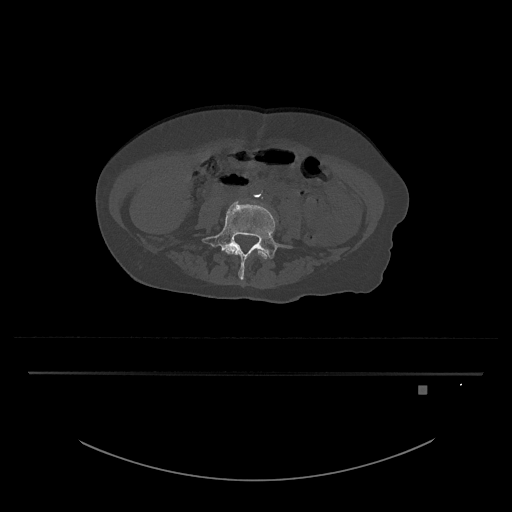
CT including the spine, one axial slice; position 319 of 797 along the scan axis; reconstruction kernel Br40s/3; bone window (W 1800 / L 400 HU); 512 × 512 image matrix. Patient: female, 57 years. Case-level facts recorded for this patient, not image findings: primary cancer: cervical.
Outlined on this slice (semi-automatically segmented with operator editing):
- L4 vertebra: bounding box [x1, y1, x2, y2] px = [224, 245, 269, 260]